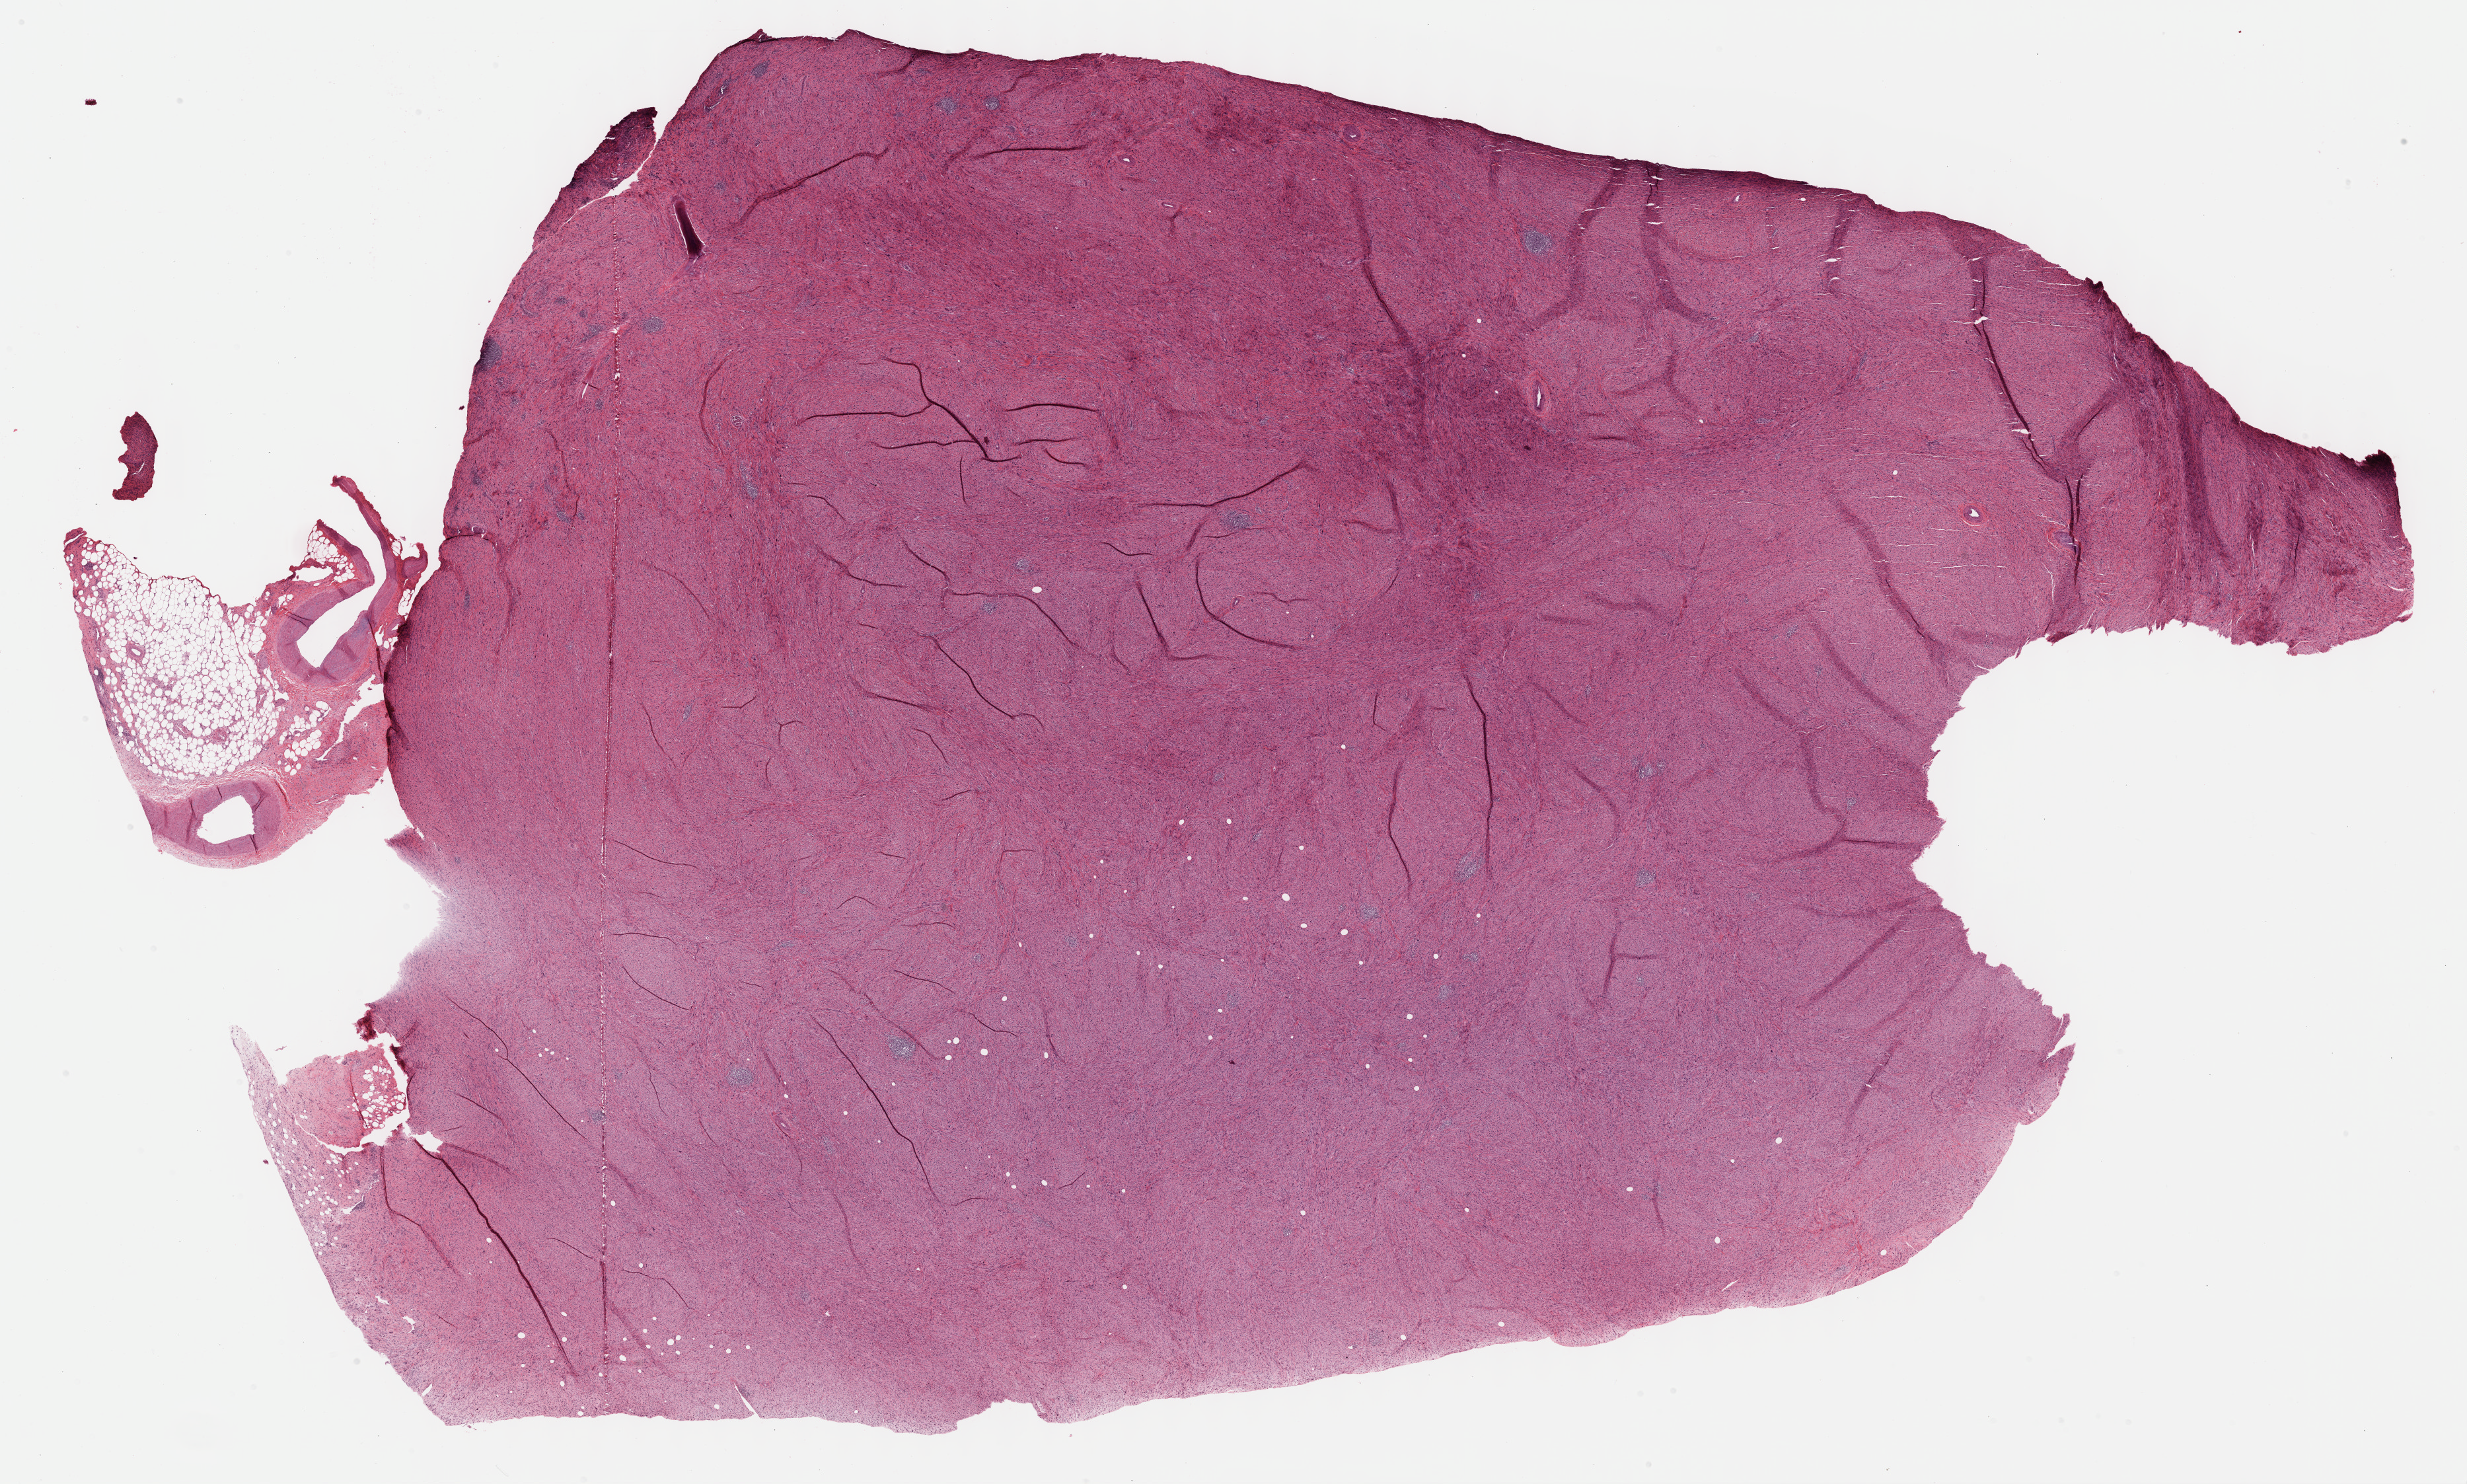
Digitized H&E-stained tissue section (whole slide) — a low-resolution overview of the entire scanned area, about 30.2 x 18.2 mm (acquisition: 40x scan), formalin-fixed paraffin-embedded (FFPE) diagnostic section, retroperitoneum and peritoneum, primary tumour sample. Male patient; age at initial diagnosis 74 years.
- pathologic diagnosis: Dedifferentiated liposarcoma (retroperitoneum)